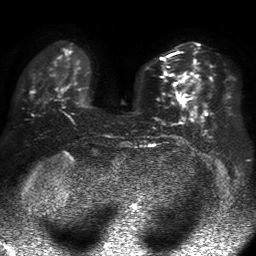
Breast MRI, one axial slice. Slice 18 of 50 in the series (ordered by position). Diffusion-weighted series; image 2 of 4 stored at this slice position (different b-values; order by instance number). 1.5 T. 4 mm slice thickness. 256 × 256 image matrix. Female patient.
Annotated regions visible in this slice (manually delineated by an expert):
- tumour on diffusion-weighted imaging: bounding box [x1, y1, x2, y2] px = [182, 93, 188, 101]